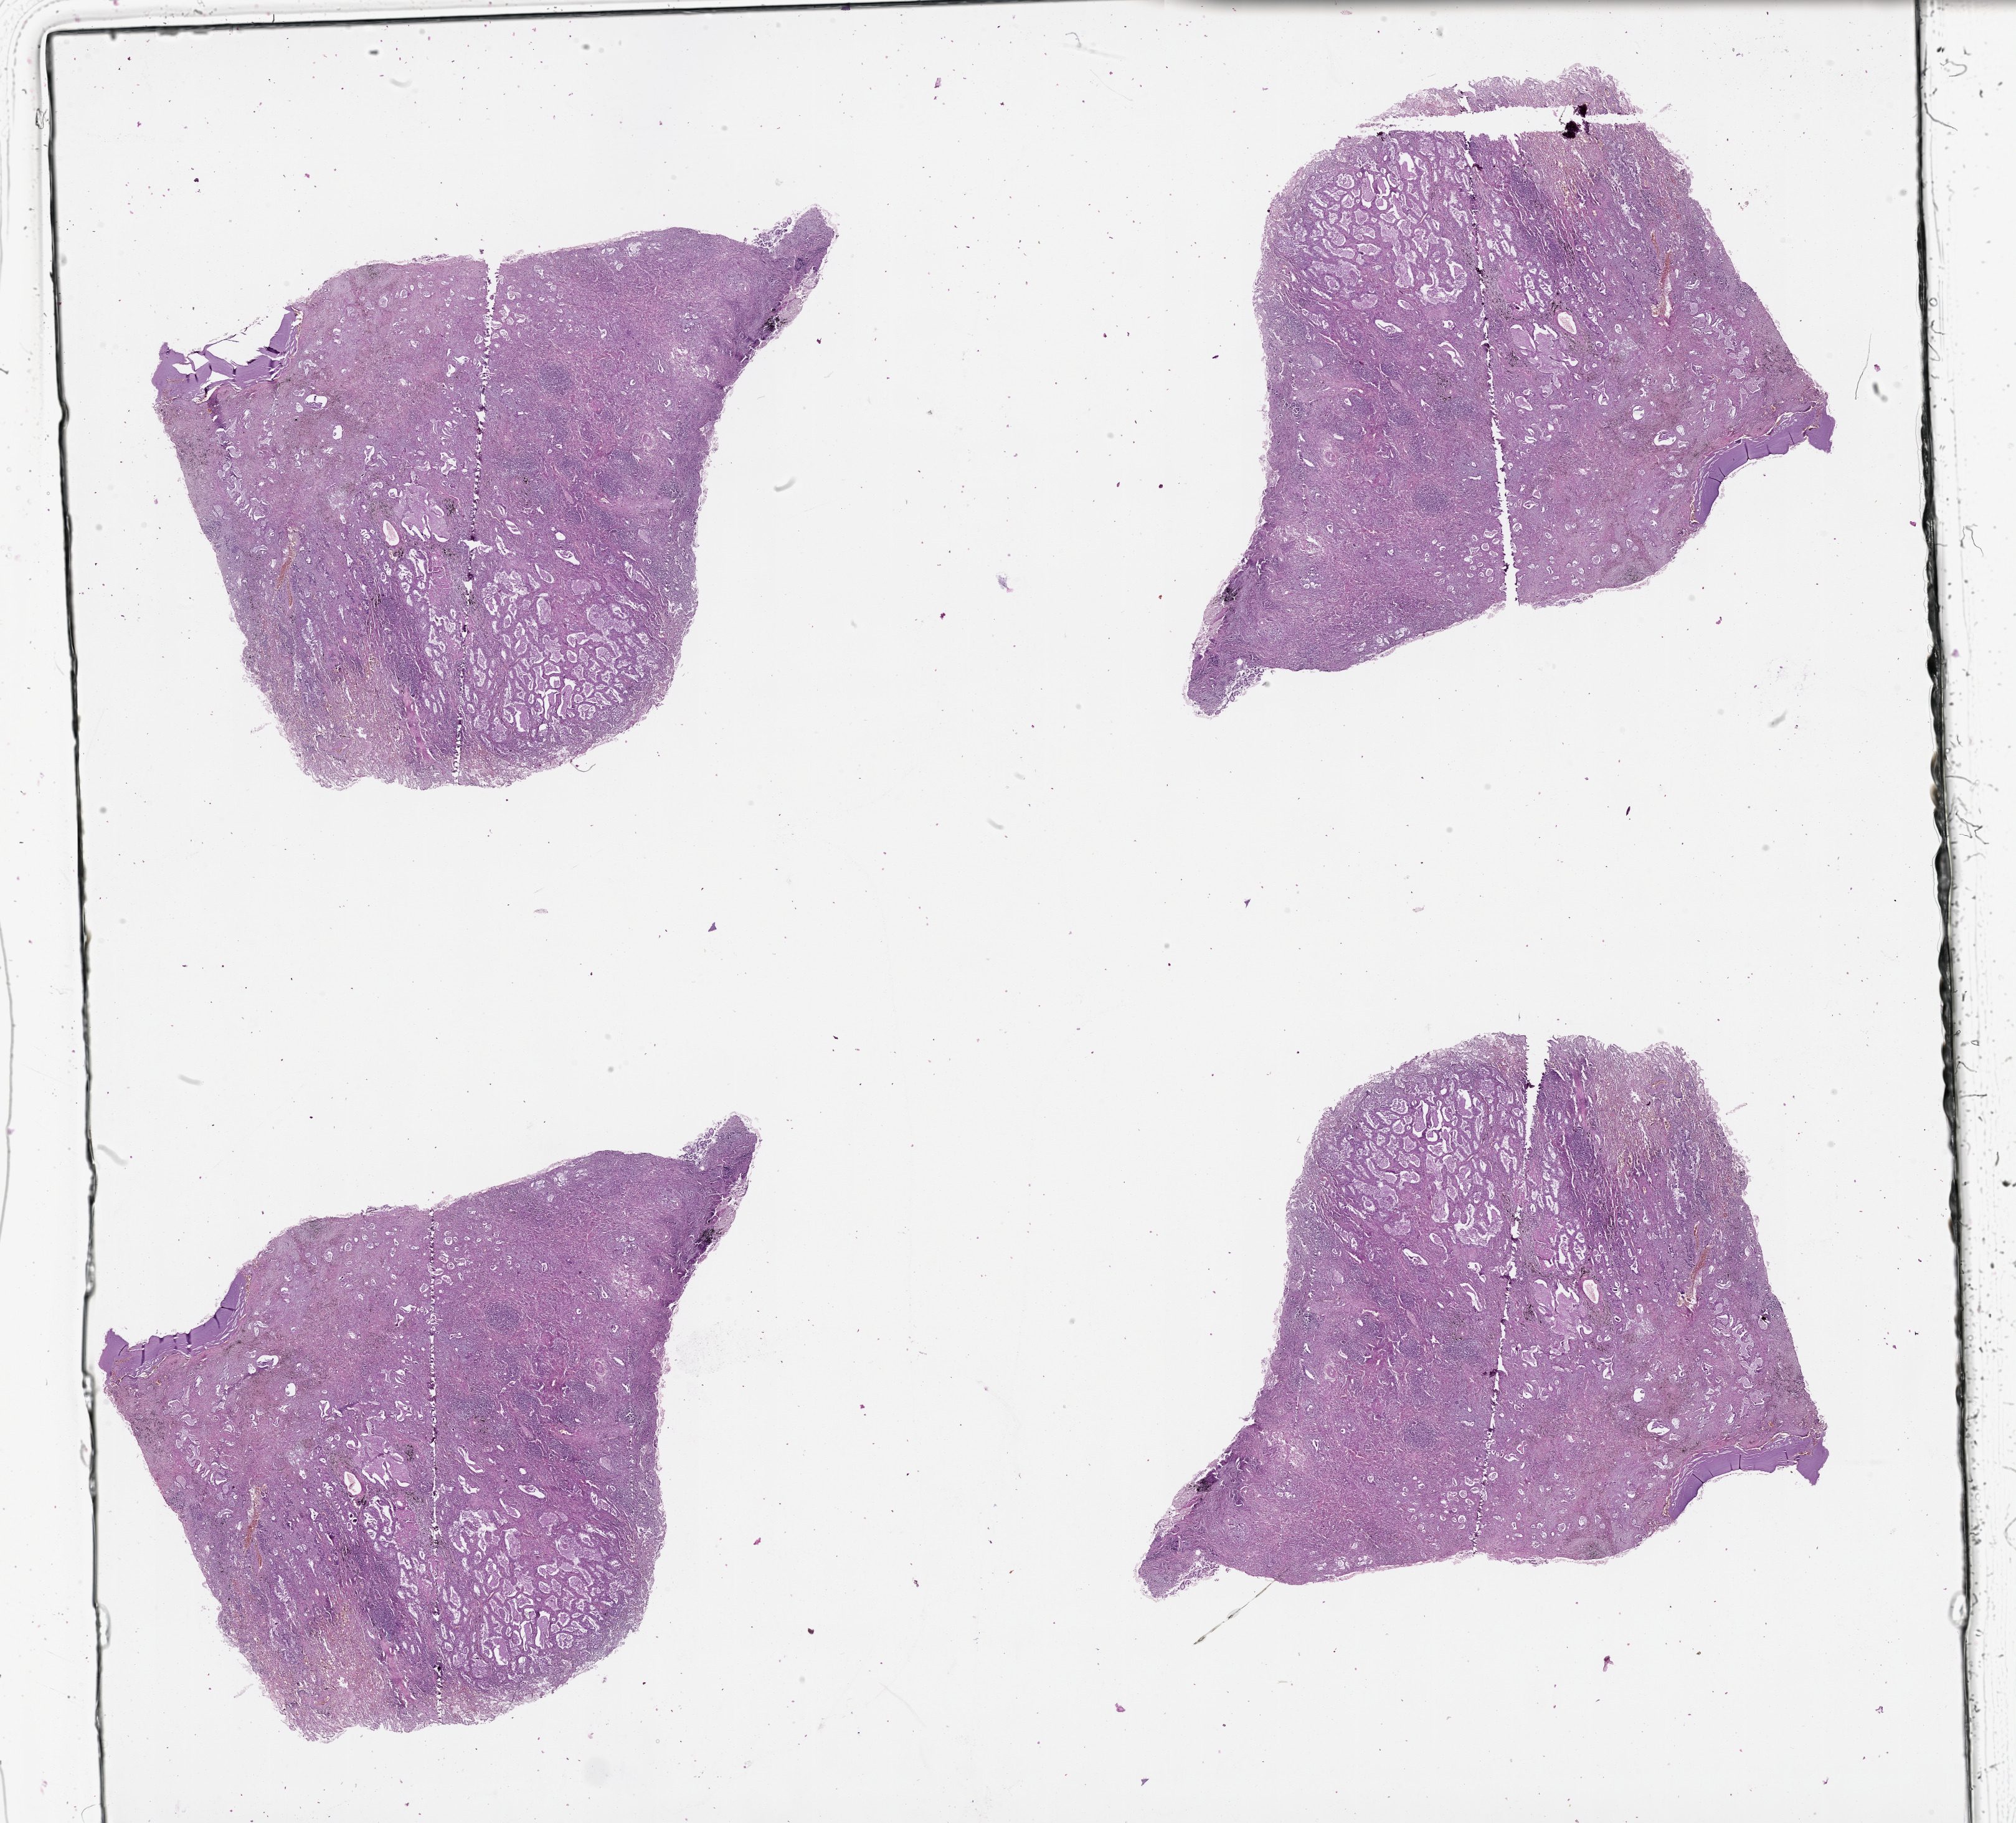
Digitized Hematoxylin and eosin (H&E) stained tissue section (whole slide) — a low-resolution overview of the entire scanned area, about 26.1 x 23.6 mm, lung, tissue type not recorded.
Patient diagnosis (cohort enrolment): lung adenocarcinoma (lung).